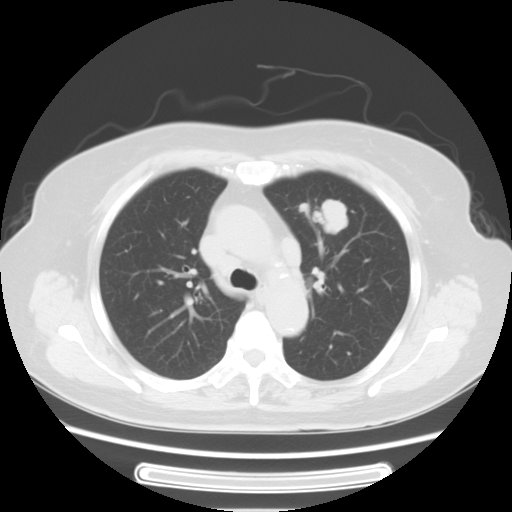
Chest CT, one axial slice; position 42 of 57 along the scan axis; lung window (W 1500 / L -600 HU); 512 × 512 image matrix, field of view 363 × 363 mm. Patient: female, 77 years. Case-level facts recorded for this patient, not image findings: clinical TNM (as recorded): T1c N3 M0.
Outlined on this slice (bounding box drawn by a radiologist):
- lung tumour (recorded histology: adenocarcinoma): bounding box [x1, y1, x2, y2] px = [295, 186, 354, 242]